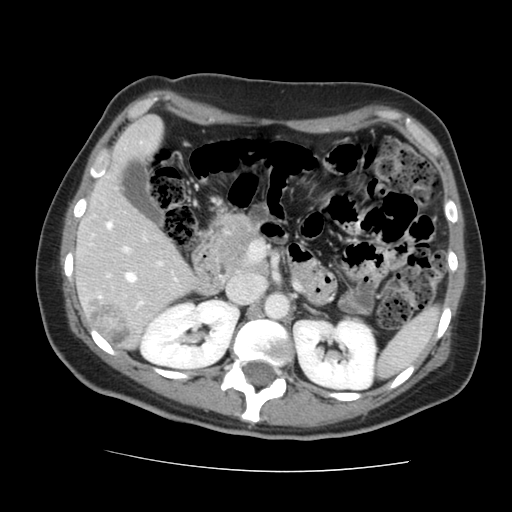
Contrast-enhanced abdominal CT, one axial slice. Position 81 of 144 along the scan axis. Soft-tissue window (W 400 / L 40 HU). 2.5 mm slice thickness. 512 × 512 image matrix, field of view 333 × 333 mm. Female patient, age 46 years. Case-level facts recorded for this patient, not image findings: diagnosis: colorectal cancer liver metastases, imaged before liver resection; multiple liver metastases: no; largest metastasis: 2.8 cm.
Structures marked on this image (outlined manually by an expert reader):
- hepatic veins: box from (x=126, y=272) to (x=137, y=282) px
- liver: (x=78, y=118)–(x=194, y=347)
- planned liver remnant (the part of the liver to remain after resection): (x=78, y=118)–(x=194, y=337)
- portal vein (with intrahepatic branches): (x=99, y=223)–(x=163, y=308)
- liver metastasis: (x=89, y=299)–(x=132, y=346)